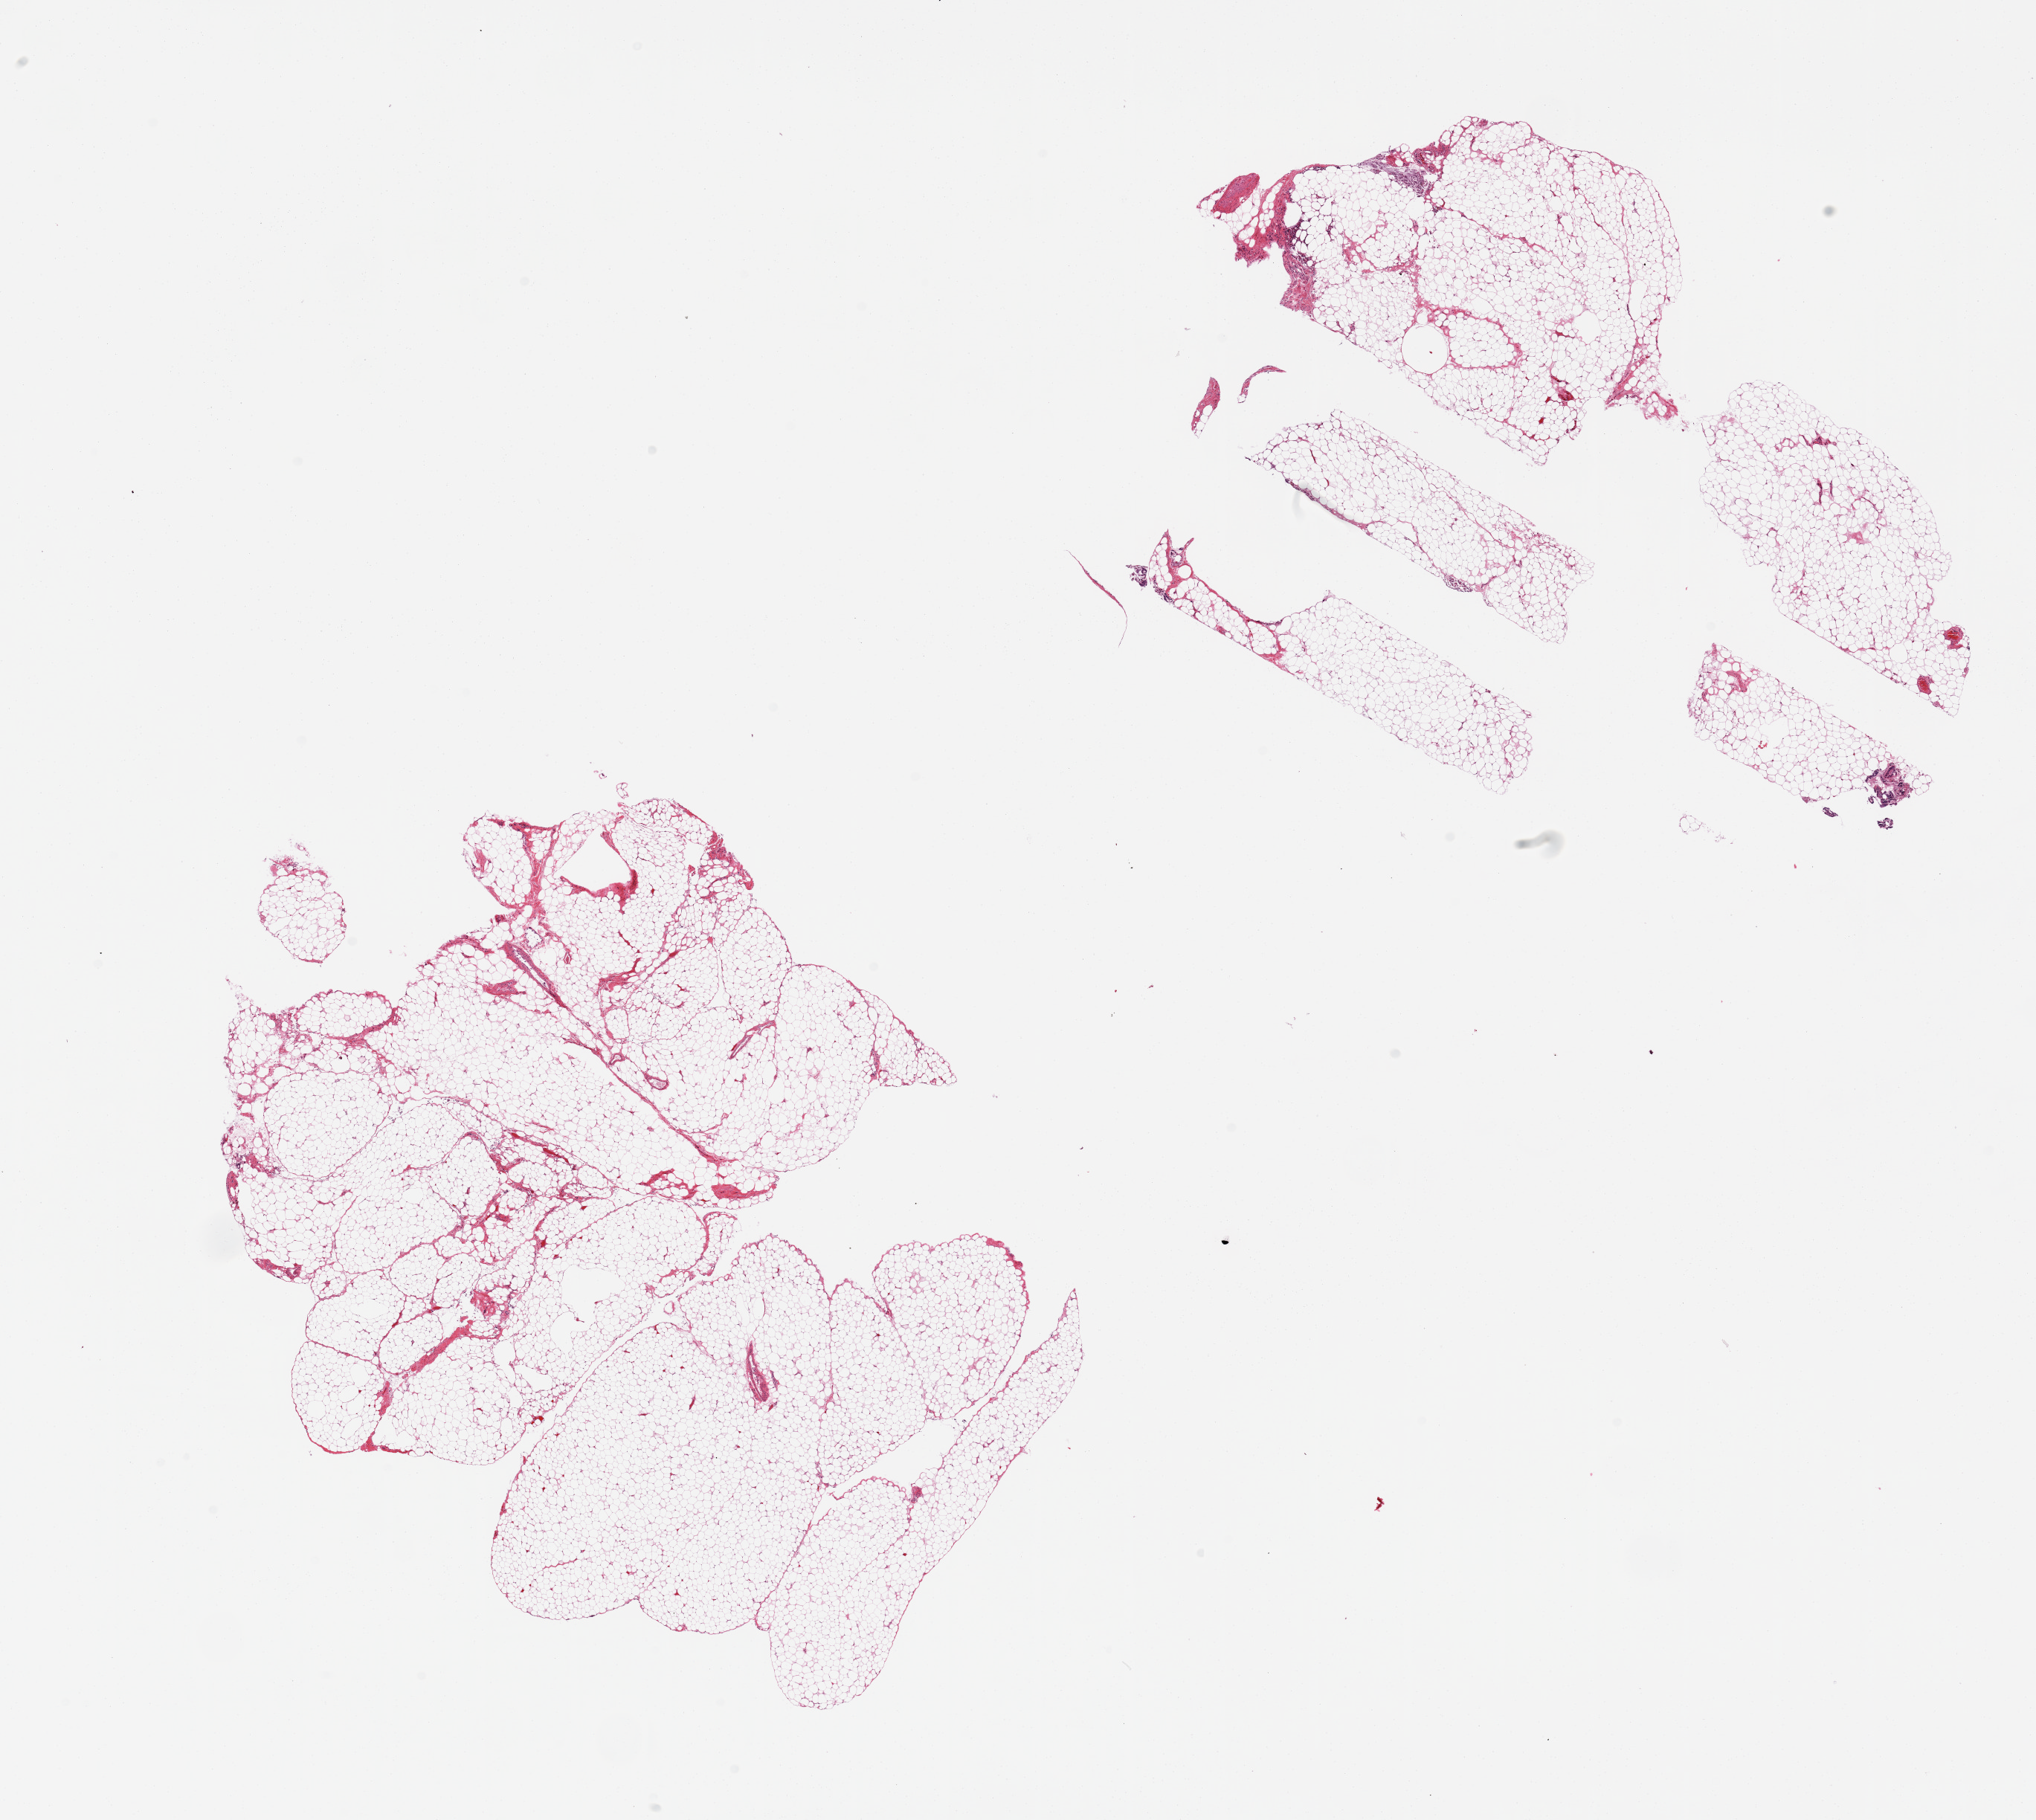
Digitized hematoxylin and eosin (H&E)-stained section, brightfield — low-resolution overview of the scanned area, about 21.7 x 19.4 mm (slide scanned at 20x). PAXgene-fixed, paraffin-embedded tissue. Sampled site (target tissue): omentum. Donor tissue sample. Donor sex: female.
Review note (as recorded): 2 pieces, minimal fibrosis.